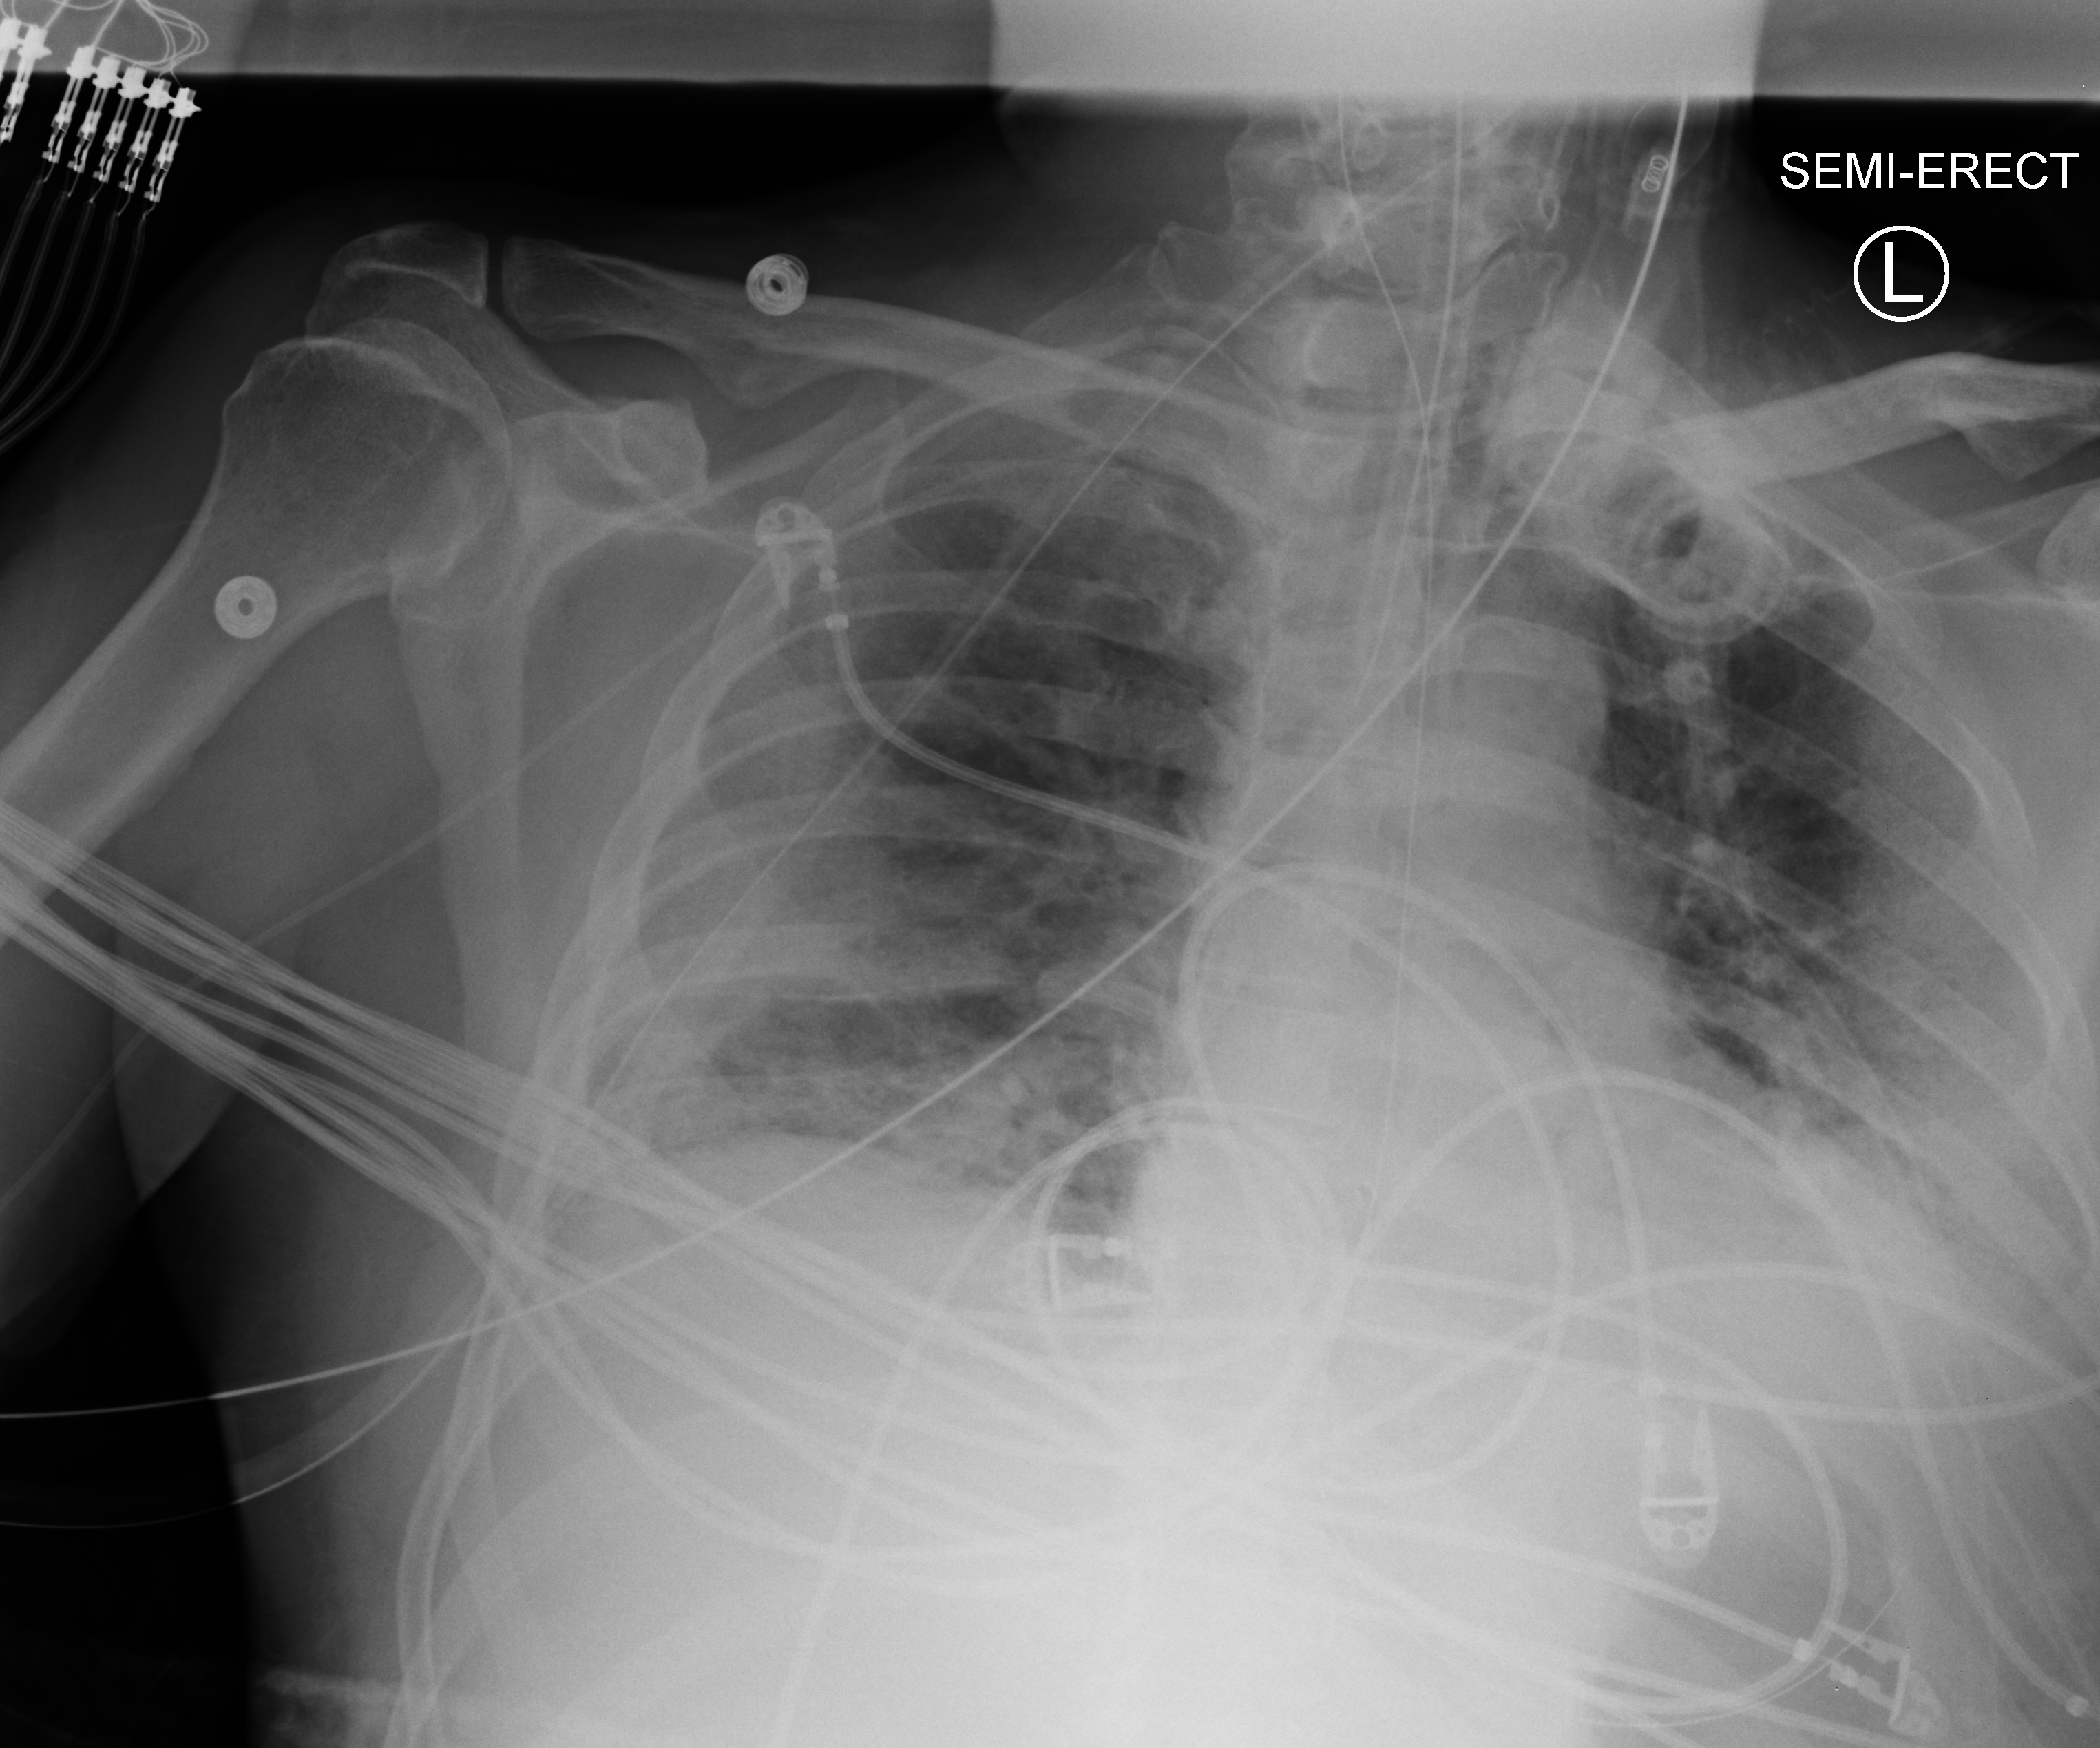
Chest X-ray (portable); anteroposterior (AP) projection. Patient hospitalised with COVID-19; male, aged 60–74 years.
Admission-level facts for this patient (not findings on this image; timing relative to this image not recorded):
- admitted to intensive care during this hospital stay: yes
- mechanically ventilated during this hospital stay: yes